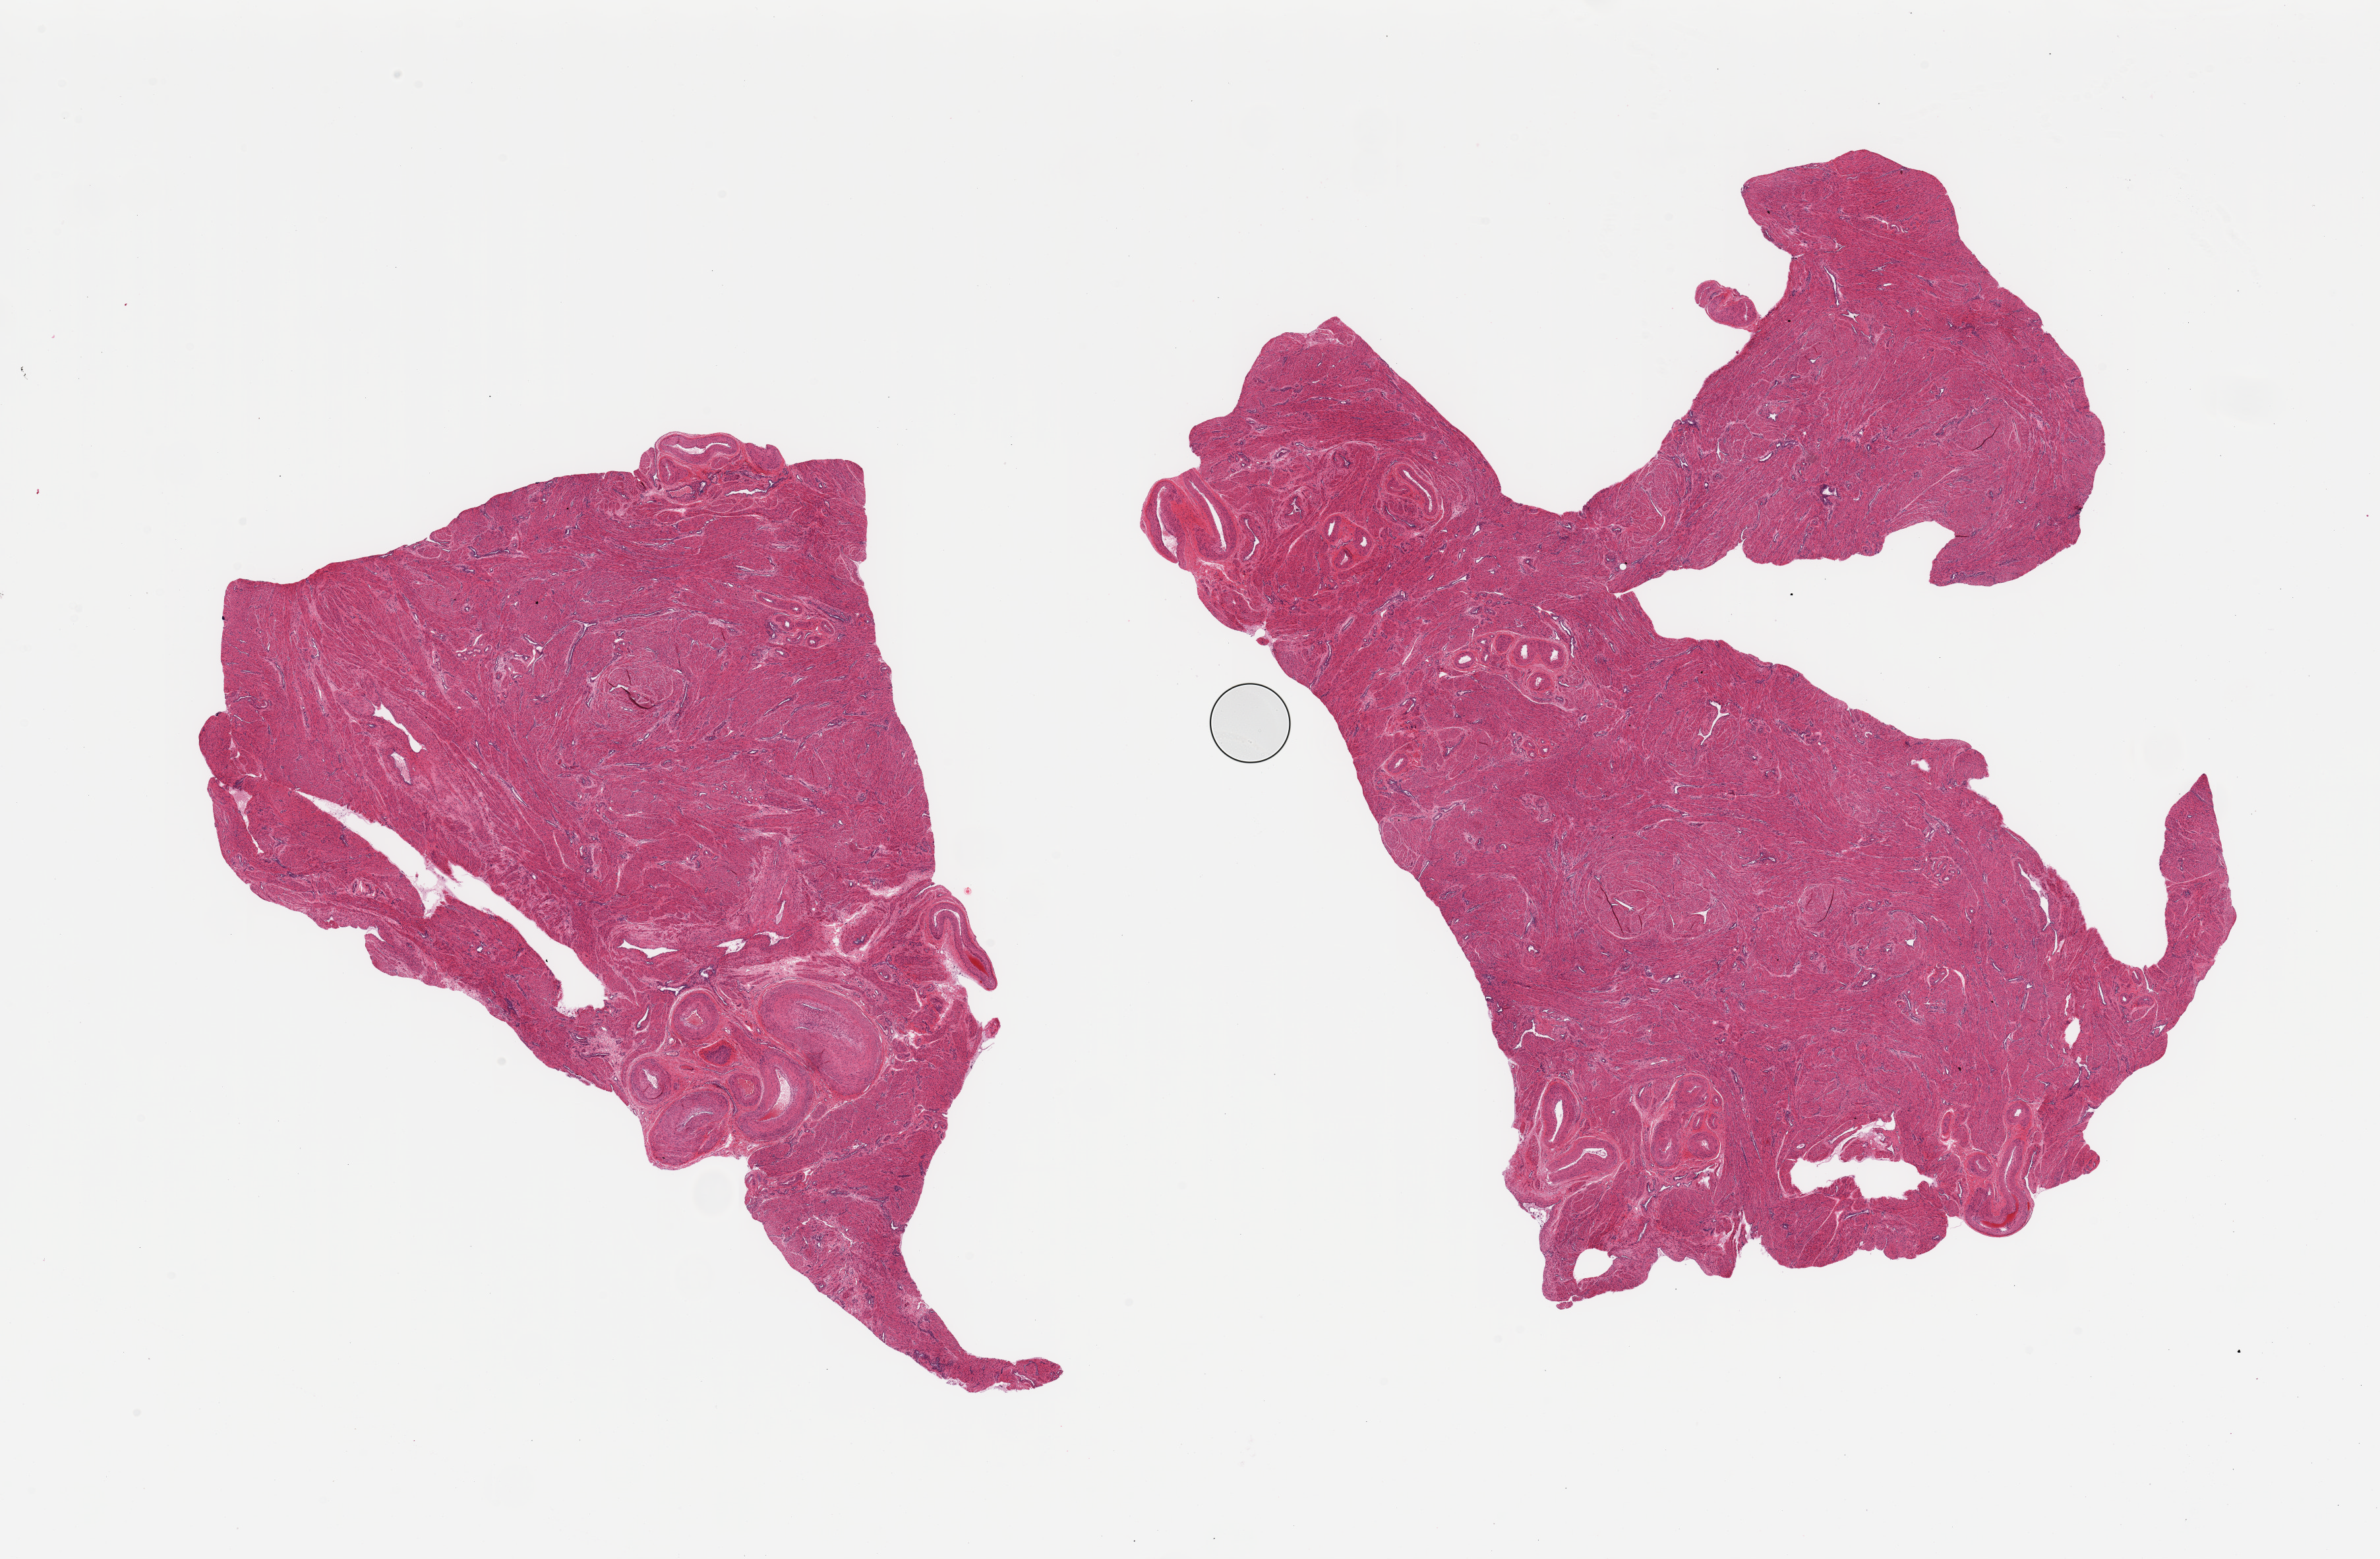
Digitized H&E-stained section — whole scanned area (about 28.5 x 18.7 mm, from a 20x scan) shown as a low-resolution overview, PAXgene-fixed, paraffin-embedded tissue, target tissue: uterus, tissue donor sample.
Pathologist's review note for this sample: 2 pieces, myometrium, no abnormalities.